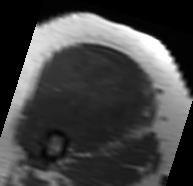
MRI of an extremity soft-tissue mass, one axial slice; slice 43 of 91 in the series (ordered by position); MR volume resampled by the dataset authors to the PET/CT grid (not the native acquisition matrix); 3.27 mm slice thickness; 193 × 186 image matrix. Female patient. From the clinical record (not read from this slice): histological type: malignant solitary fibrous tumor; grade: intermediate; site of the primary tumour: right thigh.
Structures marked on this image (expert contour drawn on MRI and transferred to this co-registered scan by the dataset authors):
- gross tumour volume including surrounding oedema: bounding box [x1, y1, x2, y2] px = [22, 46, 153, 145]
- gross tumour volume (mass): [28, 46, 148, 143]